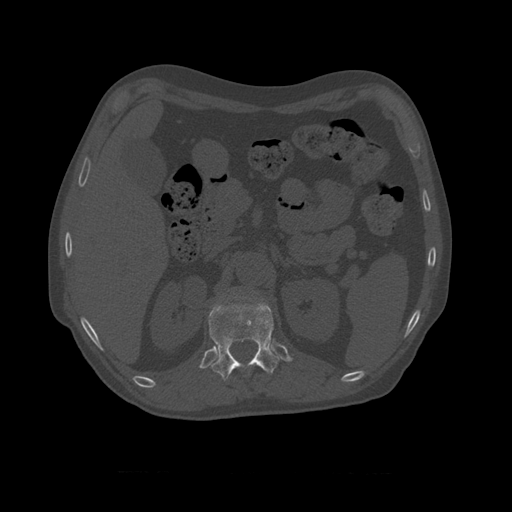
CT including the spine, one axial slice; slice 378 of 450 in the series (ordered by position); reconstruction kernel STANDARD; bone window (W 1800 / L 400 HU); 1.25 mm slice thickness; 512 × 512 image matrix, field of view 405 × 405 mm. Patient age 75 years. Case-level facts recorded for this patient, not image findings: primary cancer: prostate.
Annotated regions visible in this slice (semi-automatic segmentation, software-assisted and operator-edited):
- T11 vertebra: bounding box (x1, y1, x2, y2) in pixels: (209, 299, 280, 381)